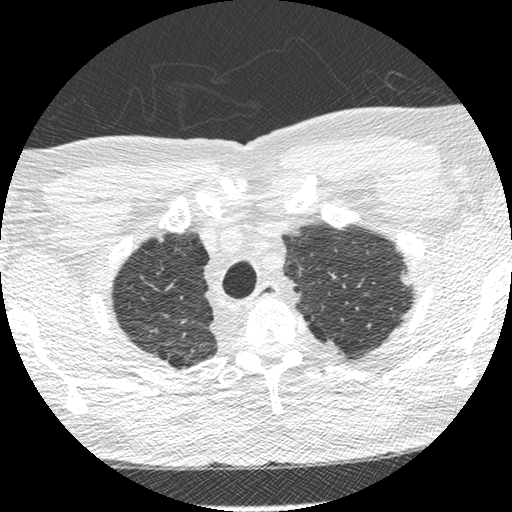
Low-dose screening chest CT, one axial slice. Position 243 of 275 along the scan axis. Reconstruction kernel STANDARD. 120 kVp. Lung window (W 1500 / L -600 HU). 1.25 mm slice thickness. 512 × 512 image matrix.
Annotated regions visible in this slice (outlined manually by an expert reader):
- lesion 1 (tumor, upper lobe of left lung): bounding box (x1, y1, x2, y2) in pixels: (401, 272, 411, 286)